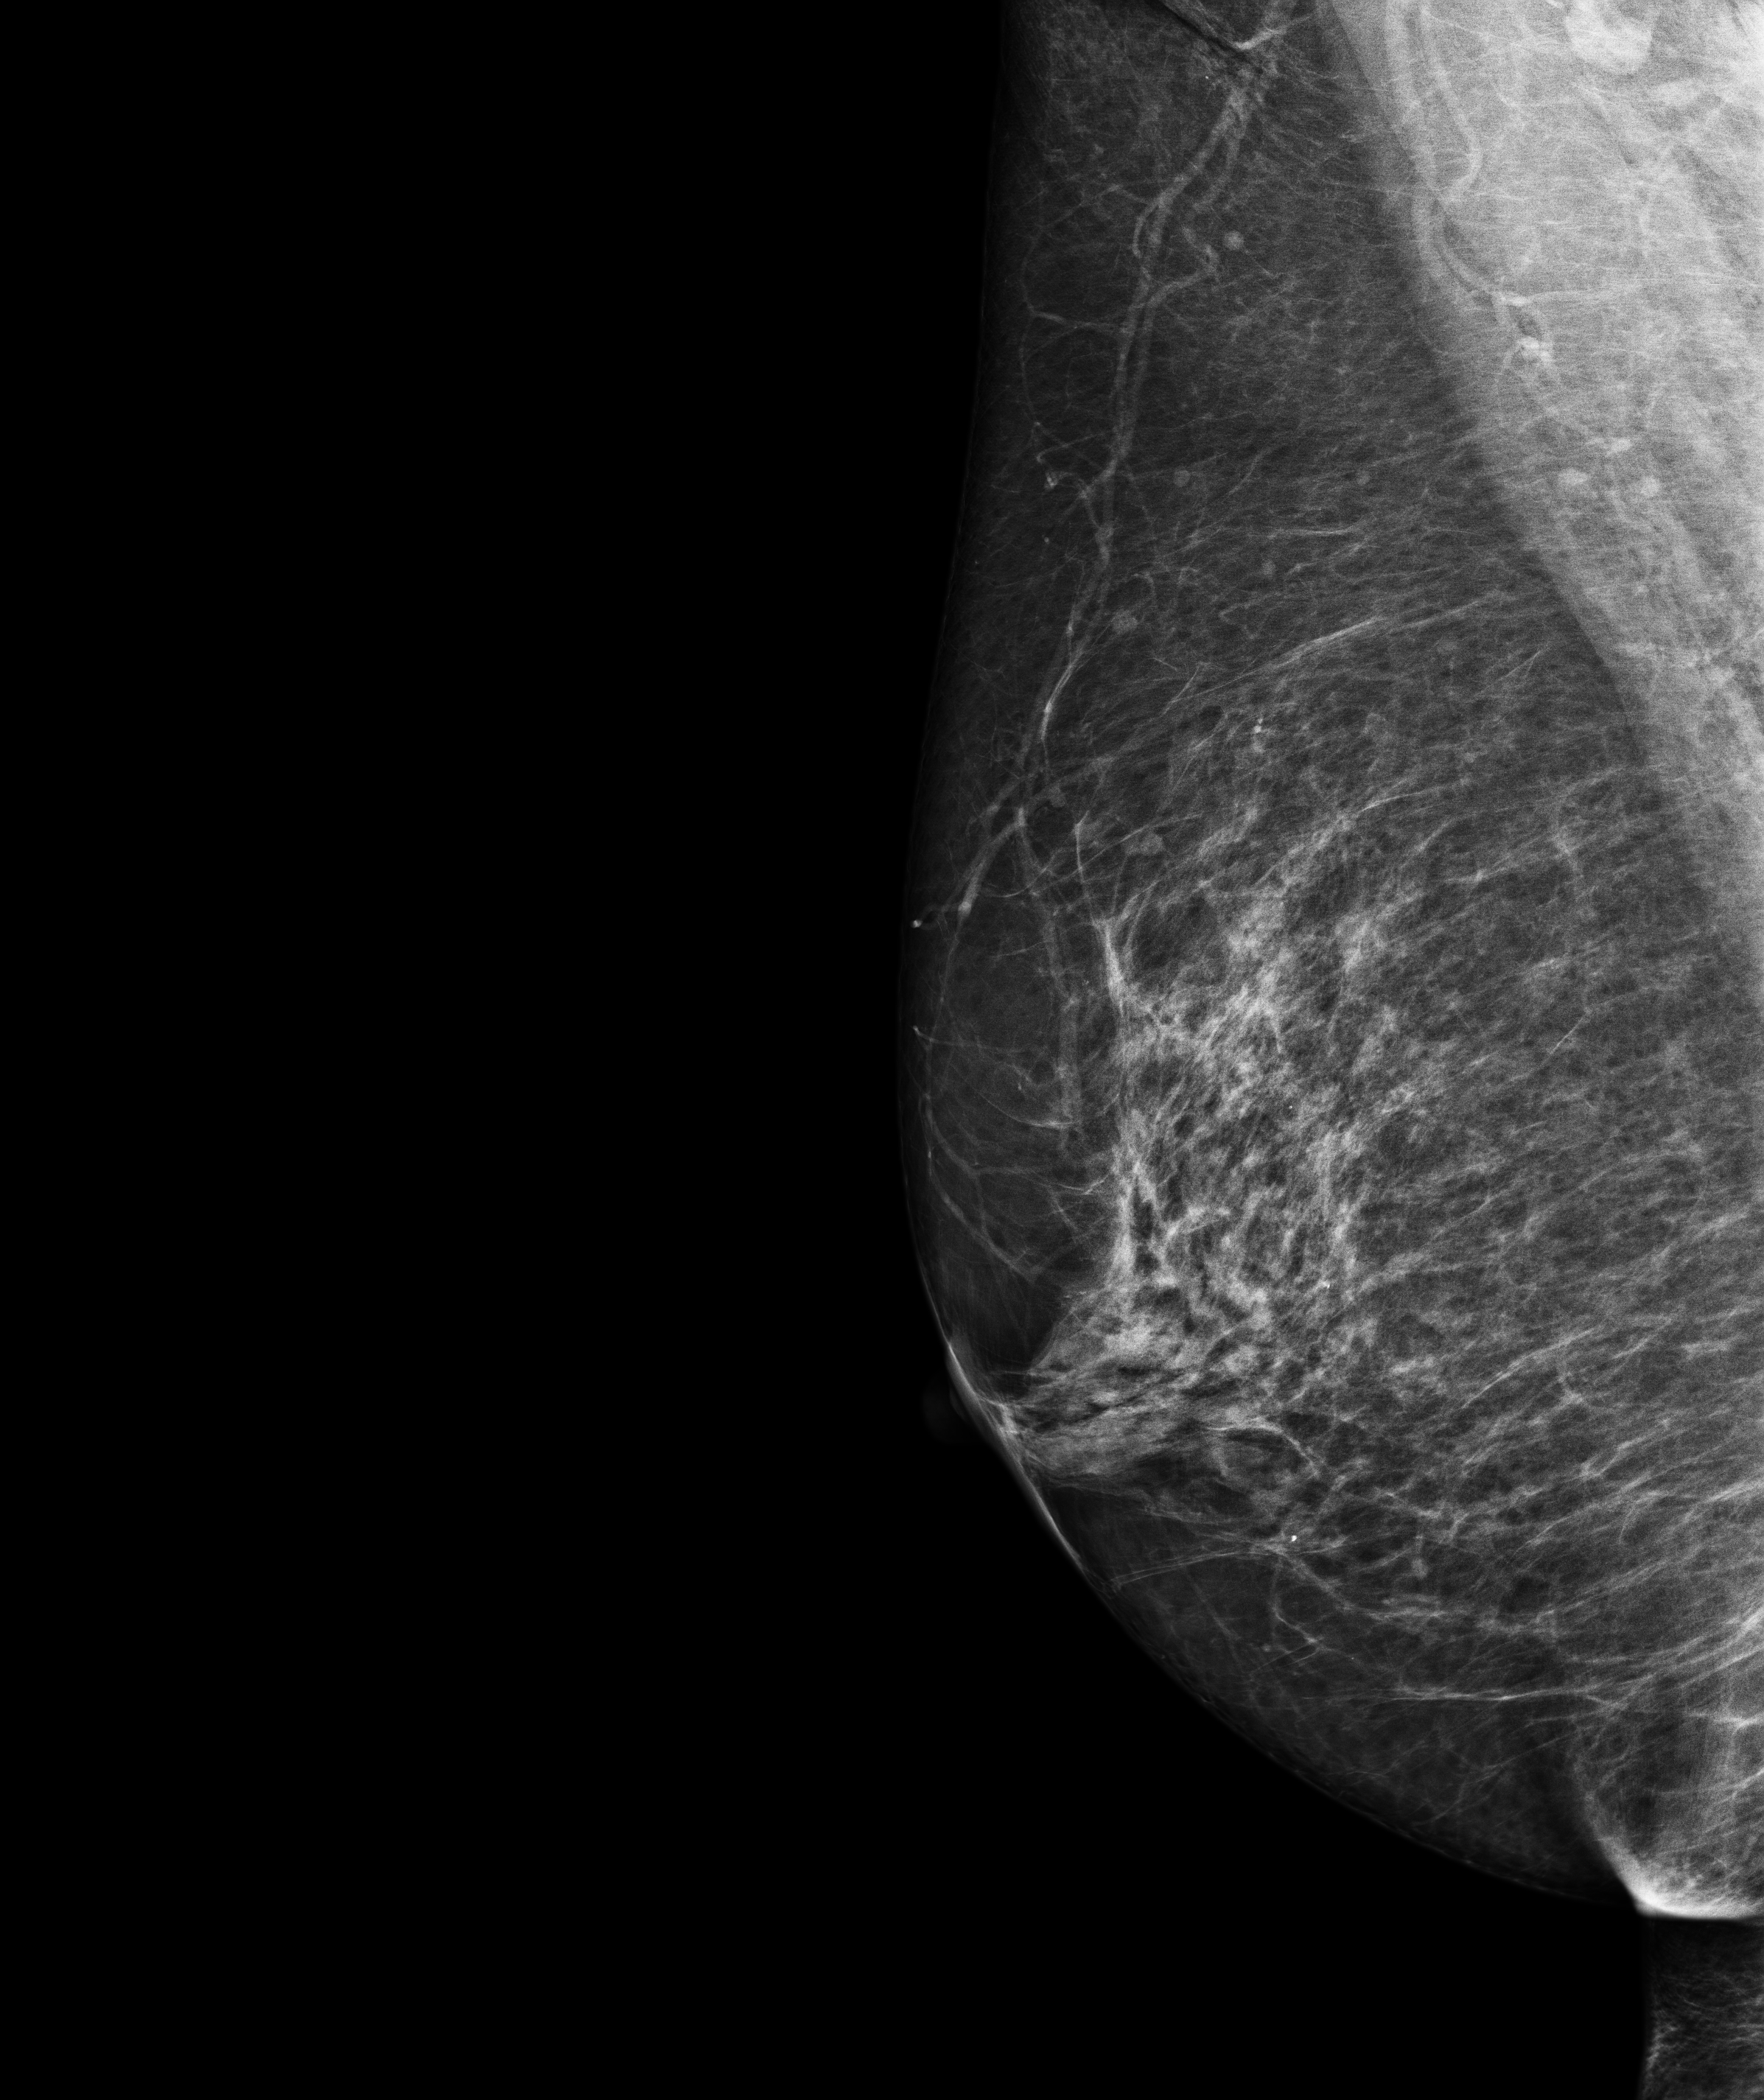
Screening examination. Patient aged 54 years (female).
Image type: full-field digital mammogram. Breast: right. Projection: mediolateral oblique (MLO) view.